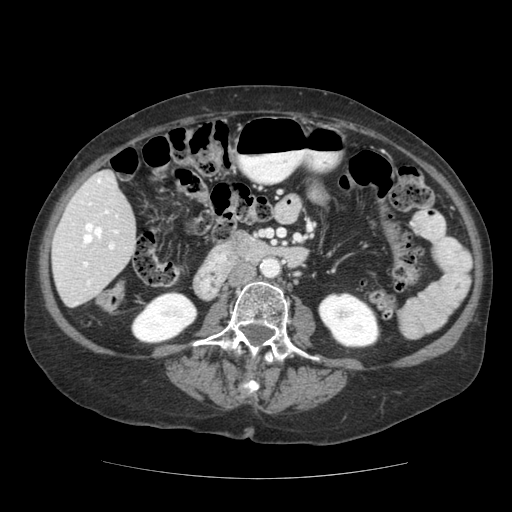
Contrast-enhanced abdominal CT (liver protocol), one axial slice; position 45 of 111 along the scan axis; reconstruction kernel STANDARD; soft-tissue window (W 400 / L 40 HU); 2.5 mm slice thickness; 512 × 512 image matrix, field of view 360 × 360 mm. Case-level facts recorded for this patient, not image findings: diagnosis: hepatocellular carcinoma (patient treated with transarterial chemoembolisation; whether this scan precedes or follows treatment is not stated here); TNM stage (as recorded): Stage-I; Child-Pugh class: A; tumour differentiation: moderately-poorly differentiated.
Outlined on this slice (semi-automatic segmentation, software-assisted and operator-edited):
- liver parenchyma outside the tumour (the mass and vessels are separate outlines, so this box may not span the whole liver): bounding box [x1, y1, x2, y2] px = [52, 170, 136, 306]
- liver vessels: [57, 178, 119, 304]